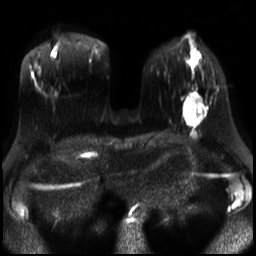
Breast MRI, one axial slice. Slice 10 of 30 in the series (ordered by position). Diffusion-weighted series; image 2 of 4 stored at this slice position (different b-values; order by instance number). 3 T. 4 mm slice thickness. 256 × 256 image matrix. Female patient.
Outlined on this slice (manually delineated by an expert):
- tumour on diffusion-weighted imaging: box from (x=184, y=93) to (x=196, y=125) px